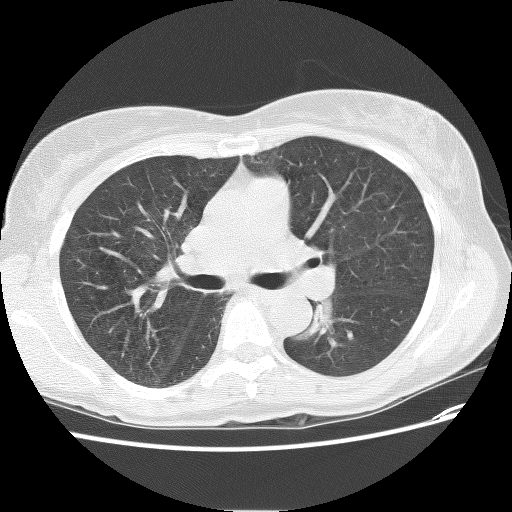
Chest CT (low-dose screening protocol), one axial image. First (baseline) screen. Lung window (W 1500 / L -600 HU). 2.5 mm slice thickness. 512 × 512 image matrix. Female participant, aged 62 years at enrolment. Former smoker at enrolment.
- Expert reader's lesion annotation, bounding box <288,299,344,343> (left, top, right, bottom; pixels).
- Screening reader's record for this exam: no non-calcified nodule ≥4 mm recorded.
- Lung cancer was diagnosed 898 days after this screen (after the third annual screen): squamous cell carcinoma, NOS, left lower lobe, stage IIIB (AJCC 6th edition), 31 mm at pathology.